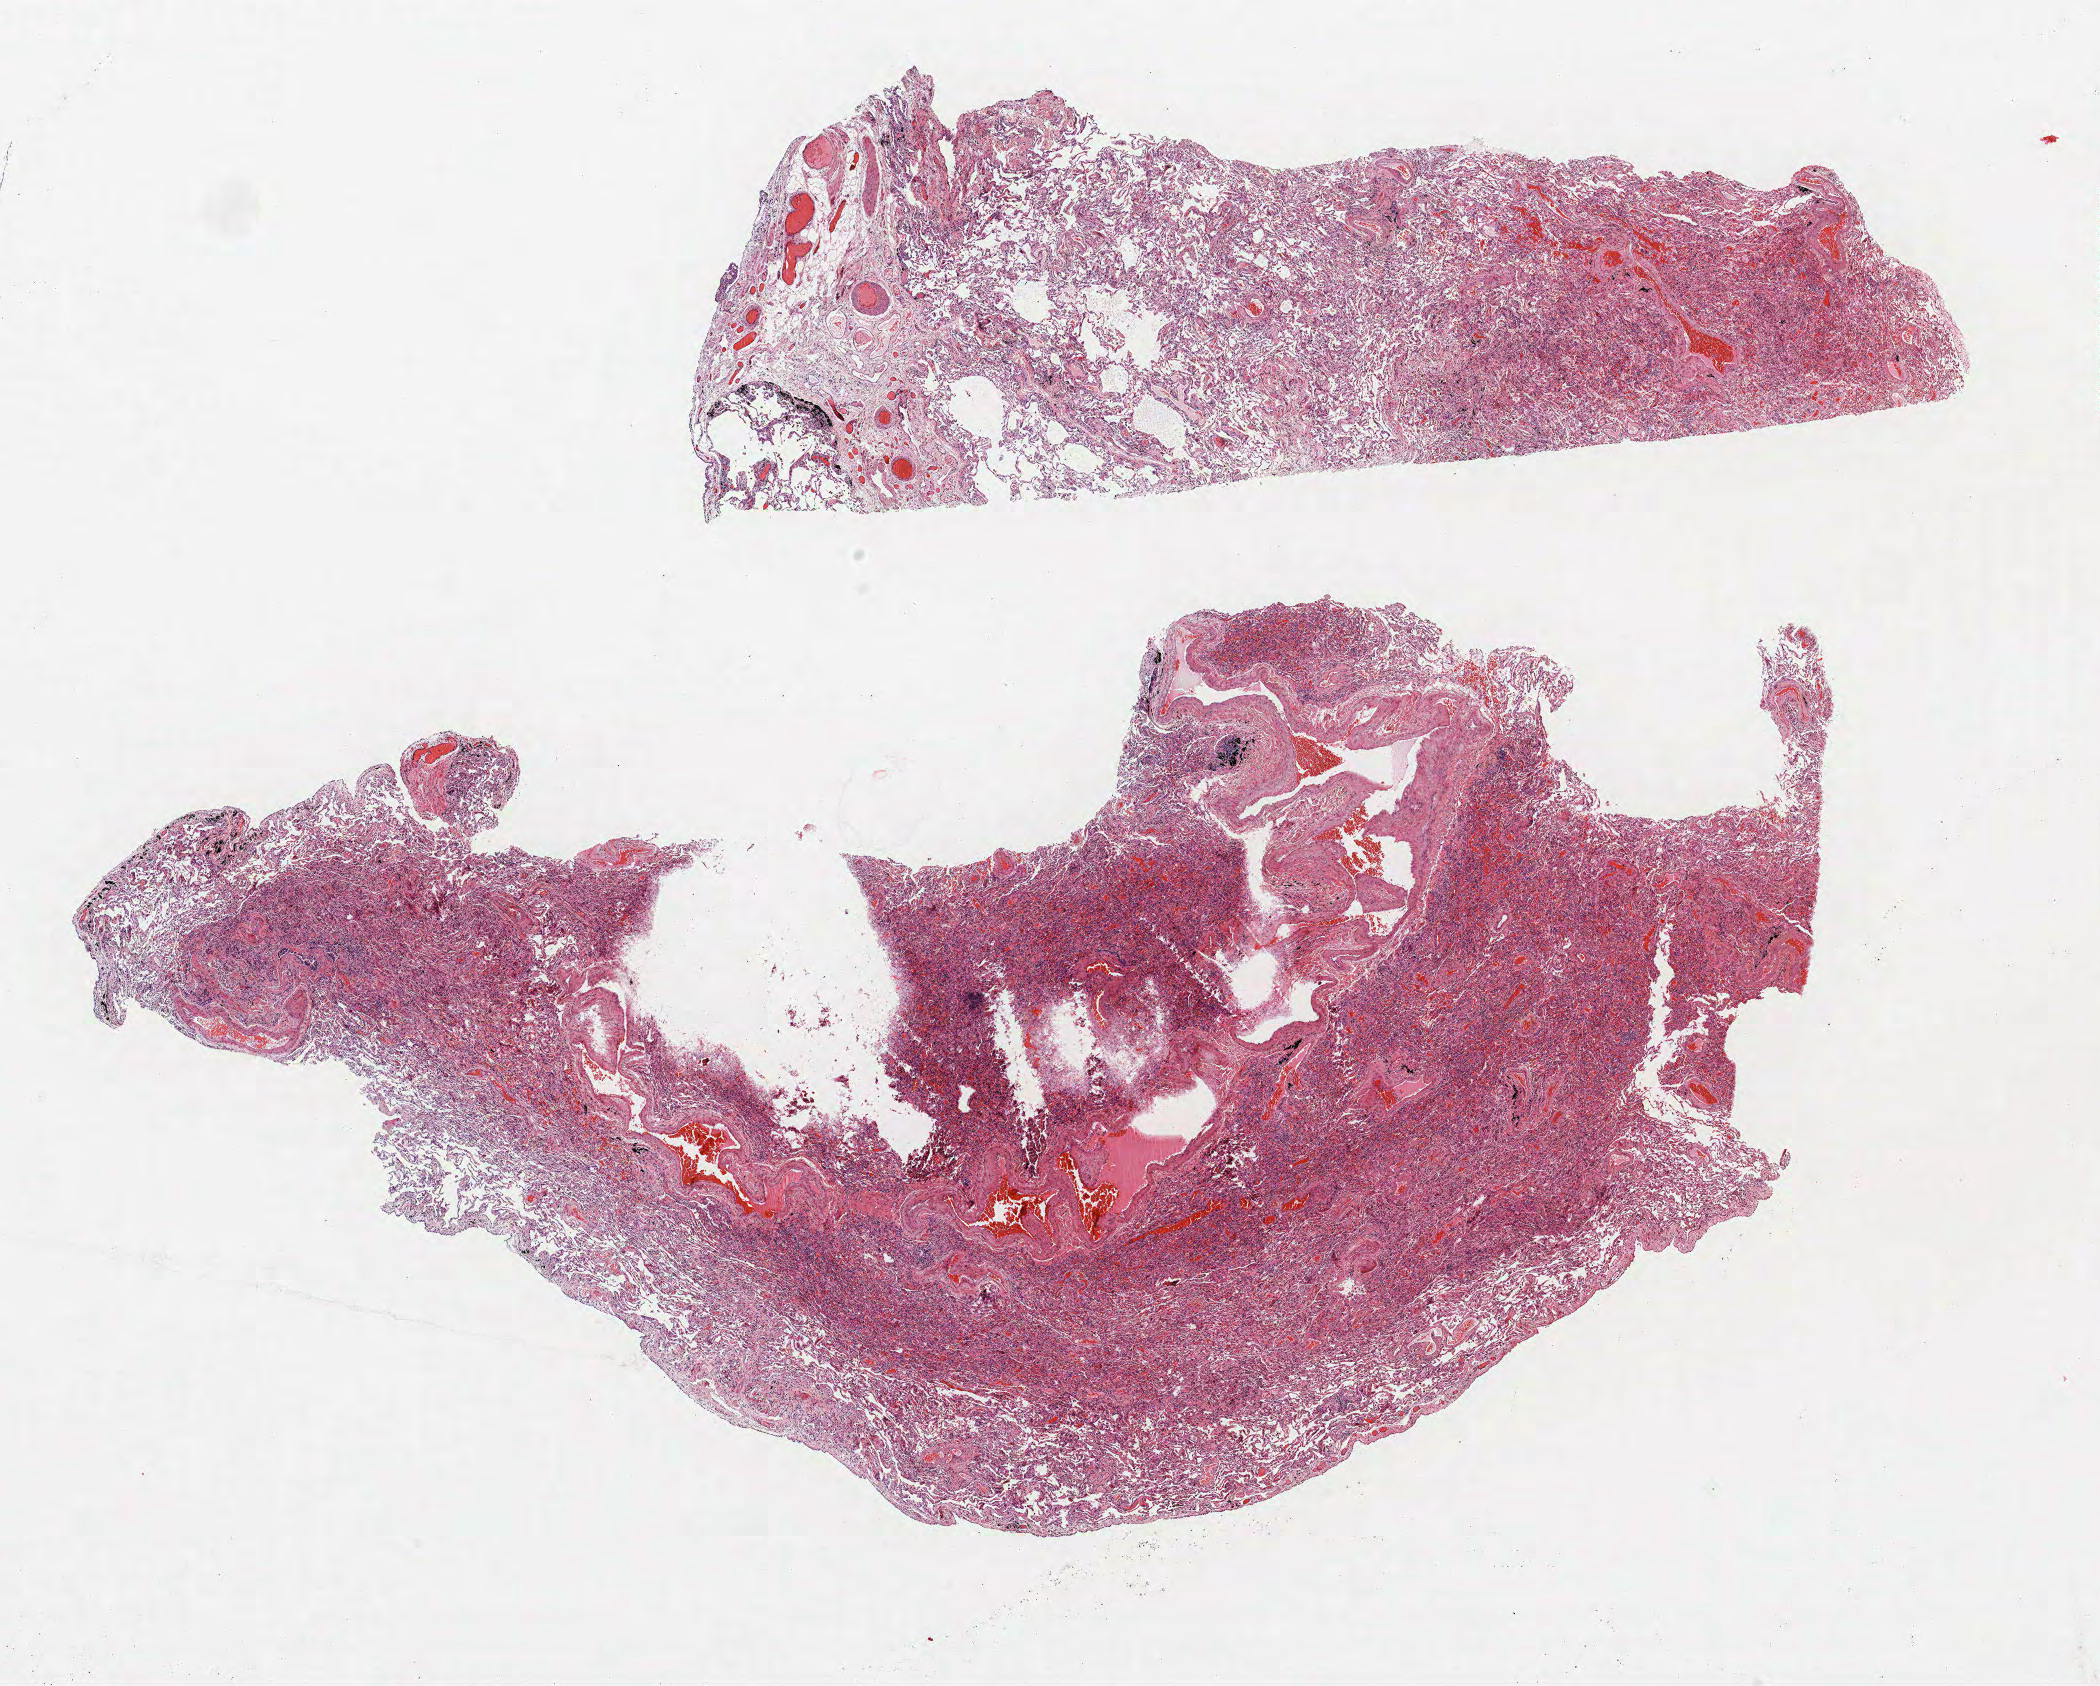
H&E-stained whole-slide image, a low-resolution overview of the entire scanned area, about 16.8 x 13.5 mm (from a 40x scan), formalin-fixed paraffin-embedded (FFPE) section, lung. Male patient, aged 74 at enrolment. Current smoker at enrolment.
Participant's lung-cancer diagnosis: Squamous cell carcinoma, NOS.